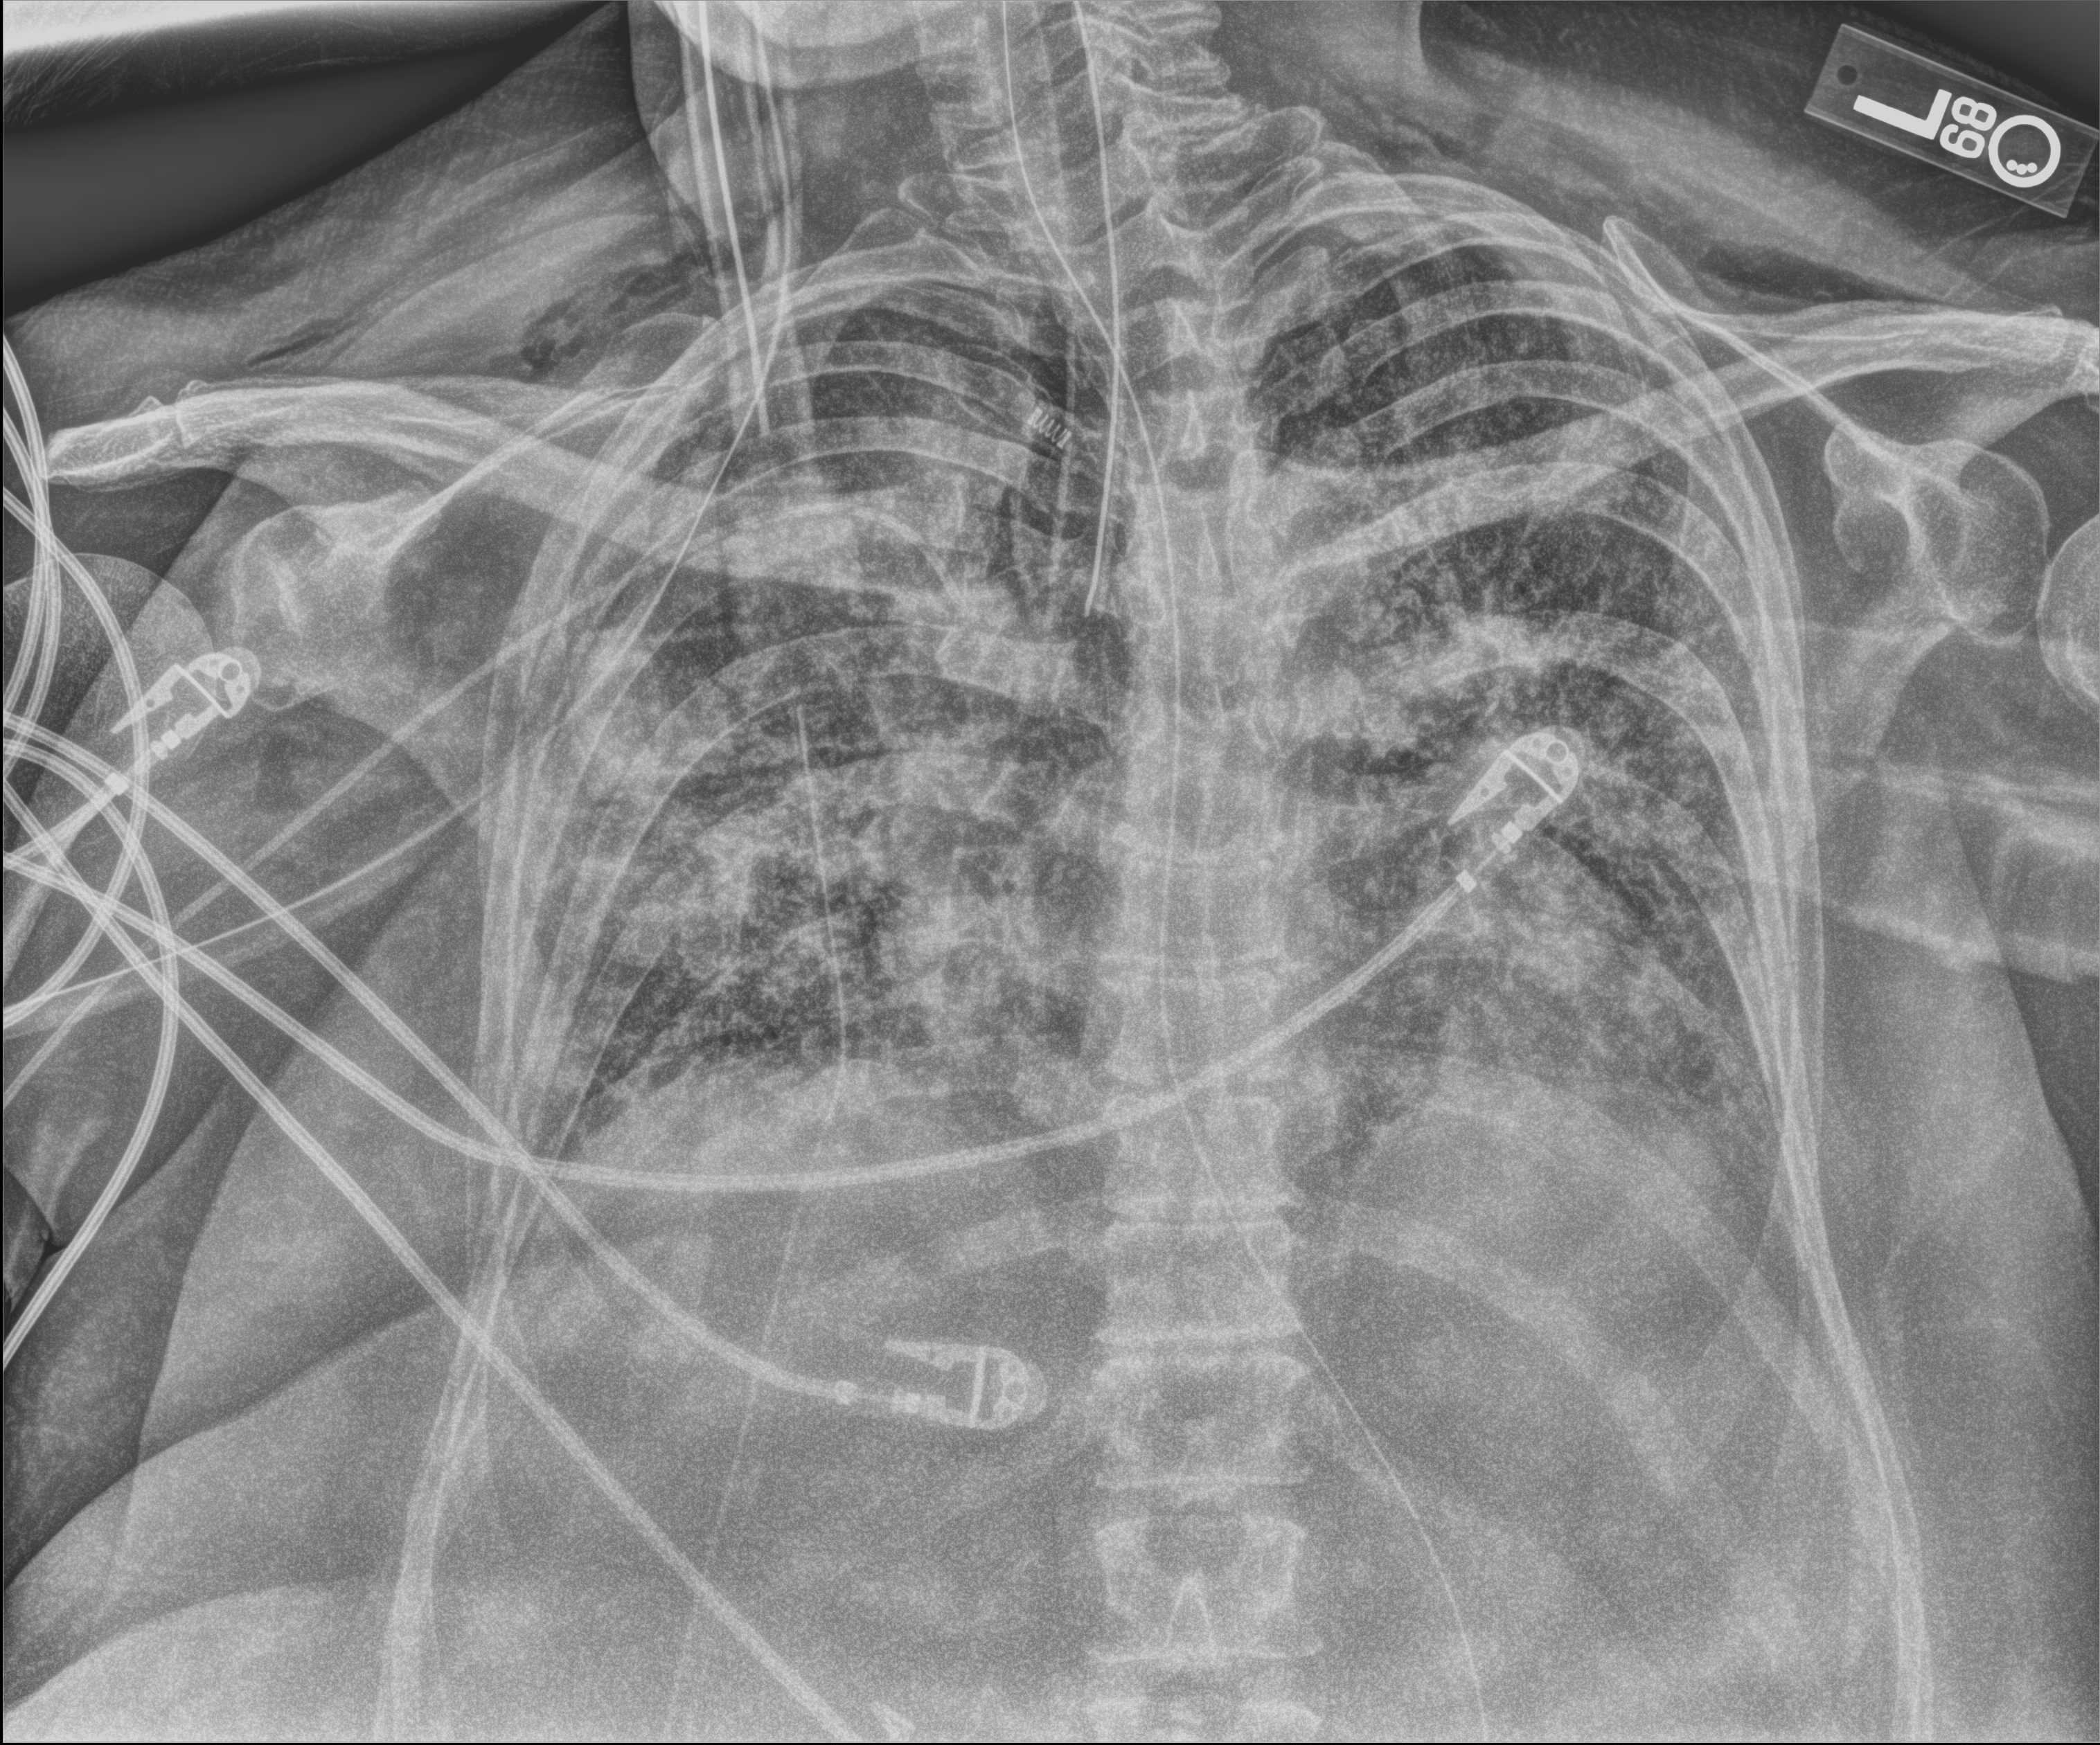
Bedside chest radiograph (computed radiography), anteroposterior (AP) projection. Patient hospitalised with COVID-19; female, aged 60–74 years.
Hospital-stay facts (about this admission, not read from this image; timing relative to this image not recorded): mechanically ventilated during this hospital stay: yes.